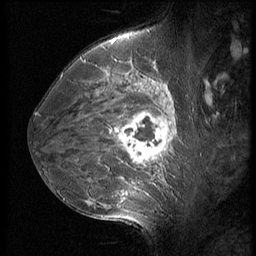
Breast MRI (dynamic contrast-enhanced), one sagittal slice; position 37 of 56 along the scan axis; 3 images stored at this slice position (order not interpretable as contrast timing); 1.5 T; TE 4.2 ms, TR 9 ms; 2.5 mm slice thickness; 256 × 256 image matrix. Female patient, age 35 years. Case-level facts recorded for this patient, not image findings: setting: breast cancer imaged before/during neoadjuvant chemotherapy; receptor status: HR-positive, HER2-negative.
Outlined on this slice (semi-automatically segmented with operator editing):
- analysis volume of interest (the breast-tissue region the enhancement analysis was run in; not a lesion): bounding box [x1, y1, x2, y2] px = [63, 60, 190, 218]
- tumour enhancement mask (voxels above the 140 % enhancement threshold inside the analysis volume of interest): [105, 76, 174, 208]